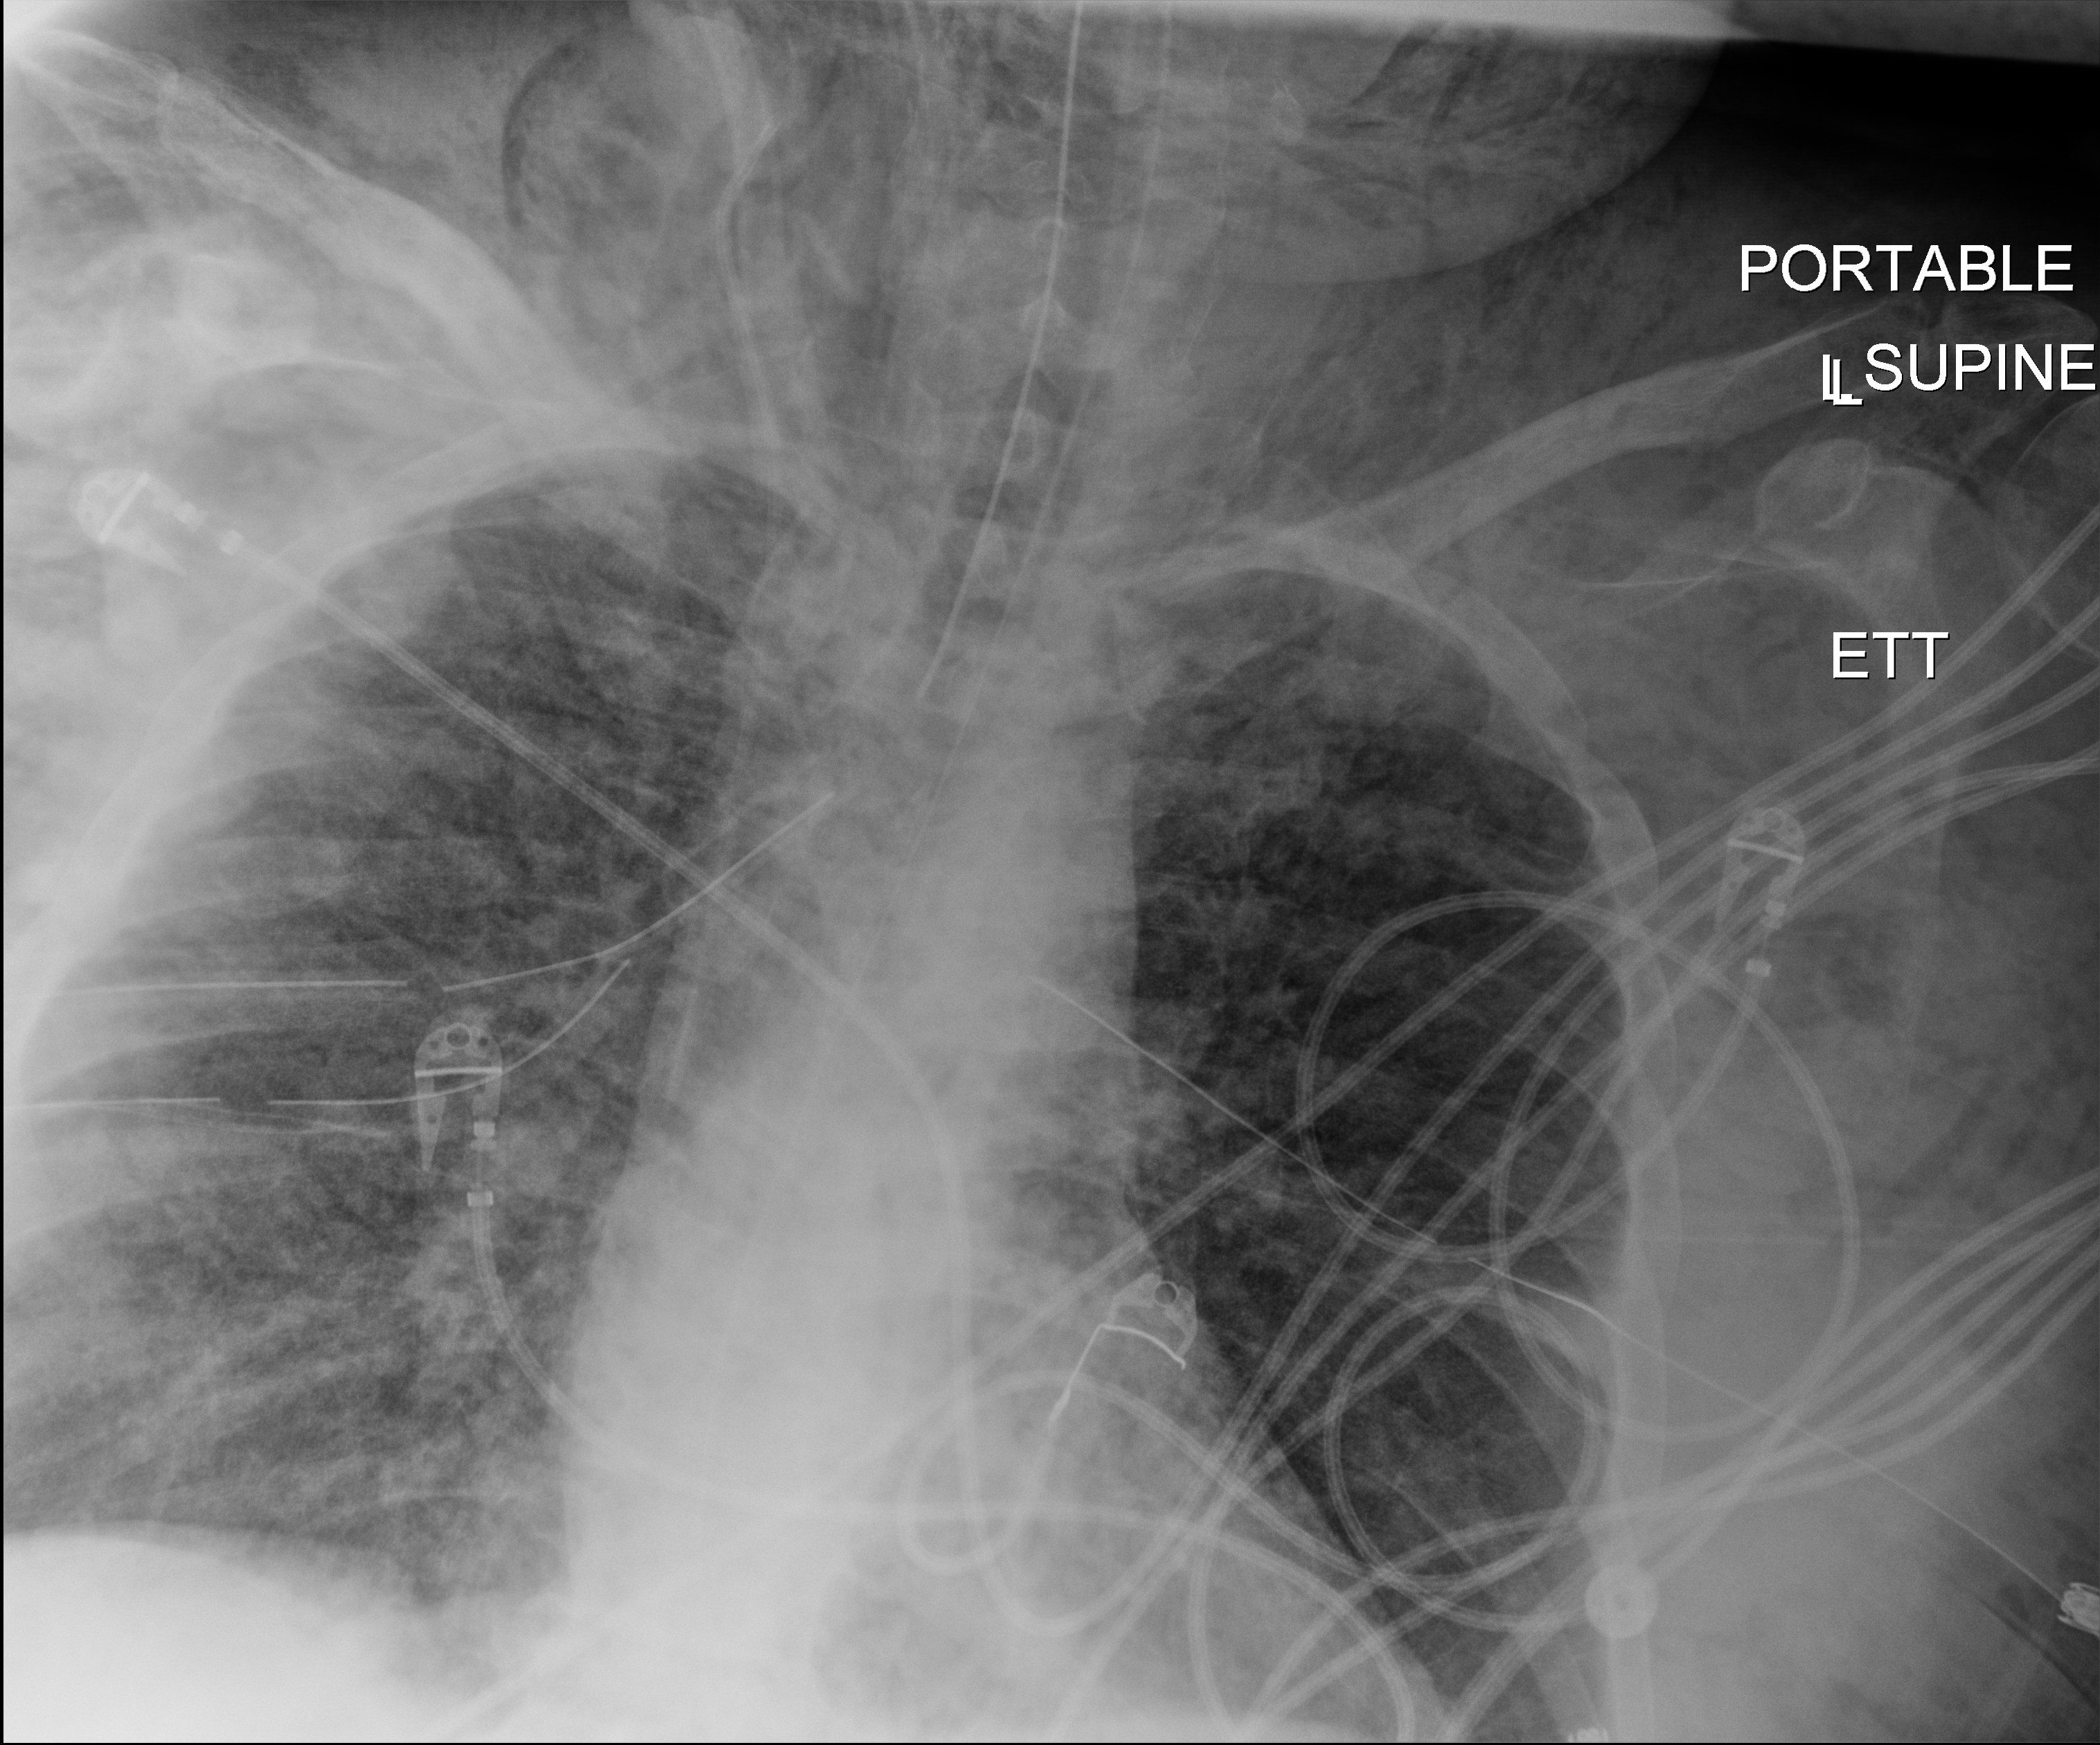
Portable chest radiograph. Patient hospitalised with COVID-19, aged 18–59 years.
Admission-level facts for this patient (not findings on this image; timing relative to this image not recorded): mechanically ventilated during this hospital stay: yes; chronic kidney disease (admission record): no.